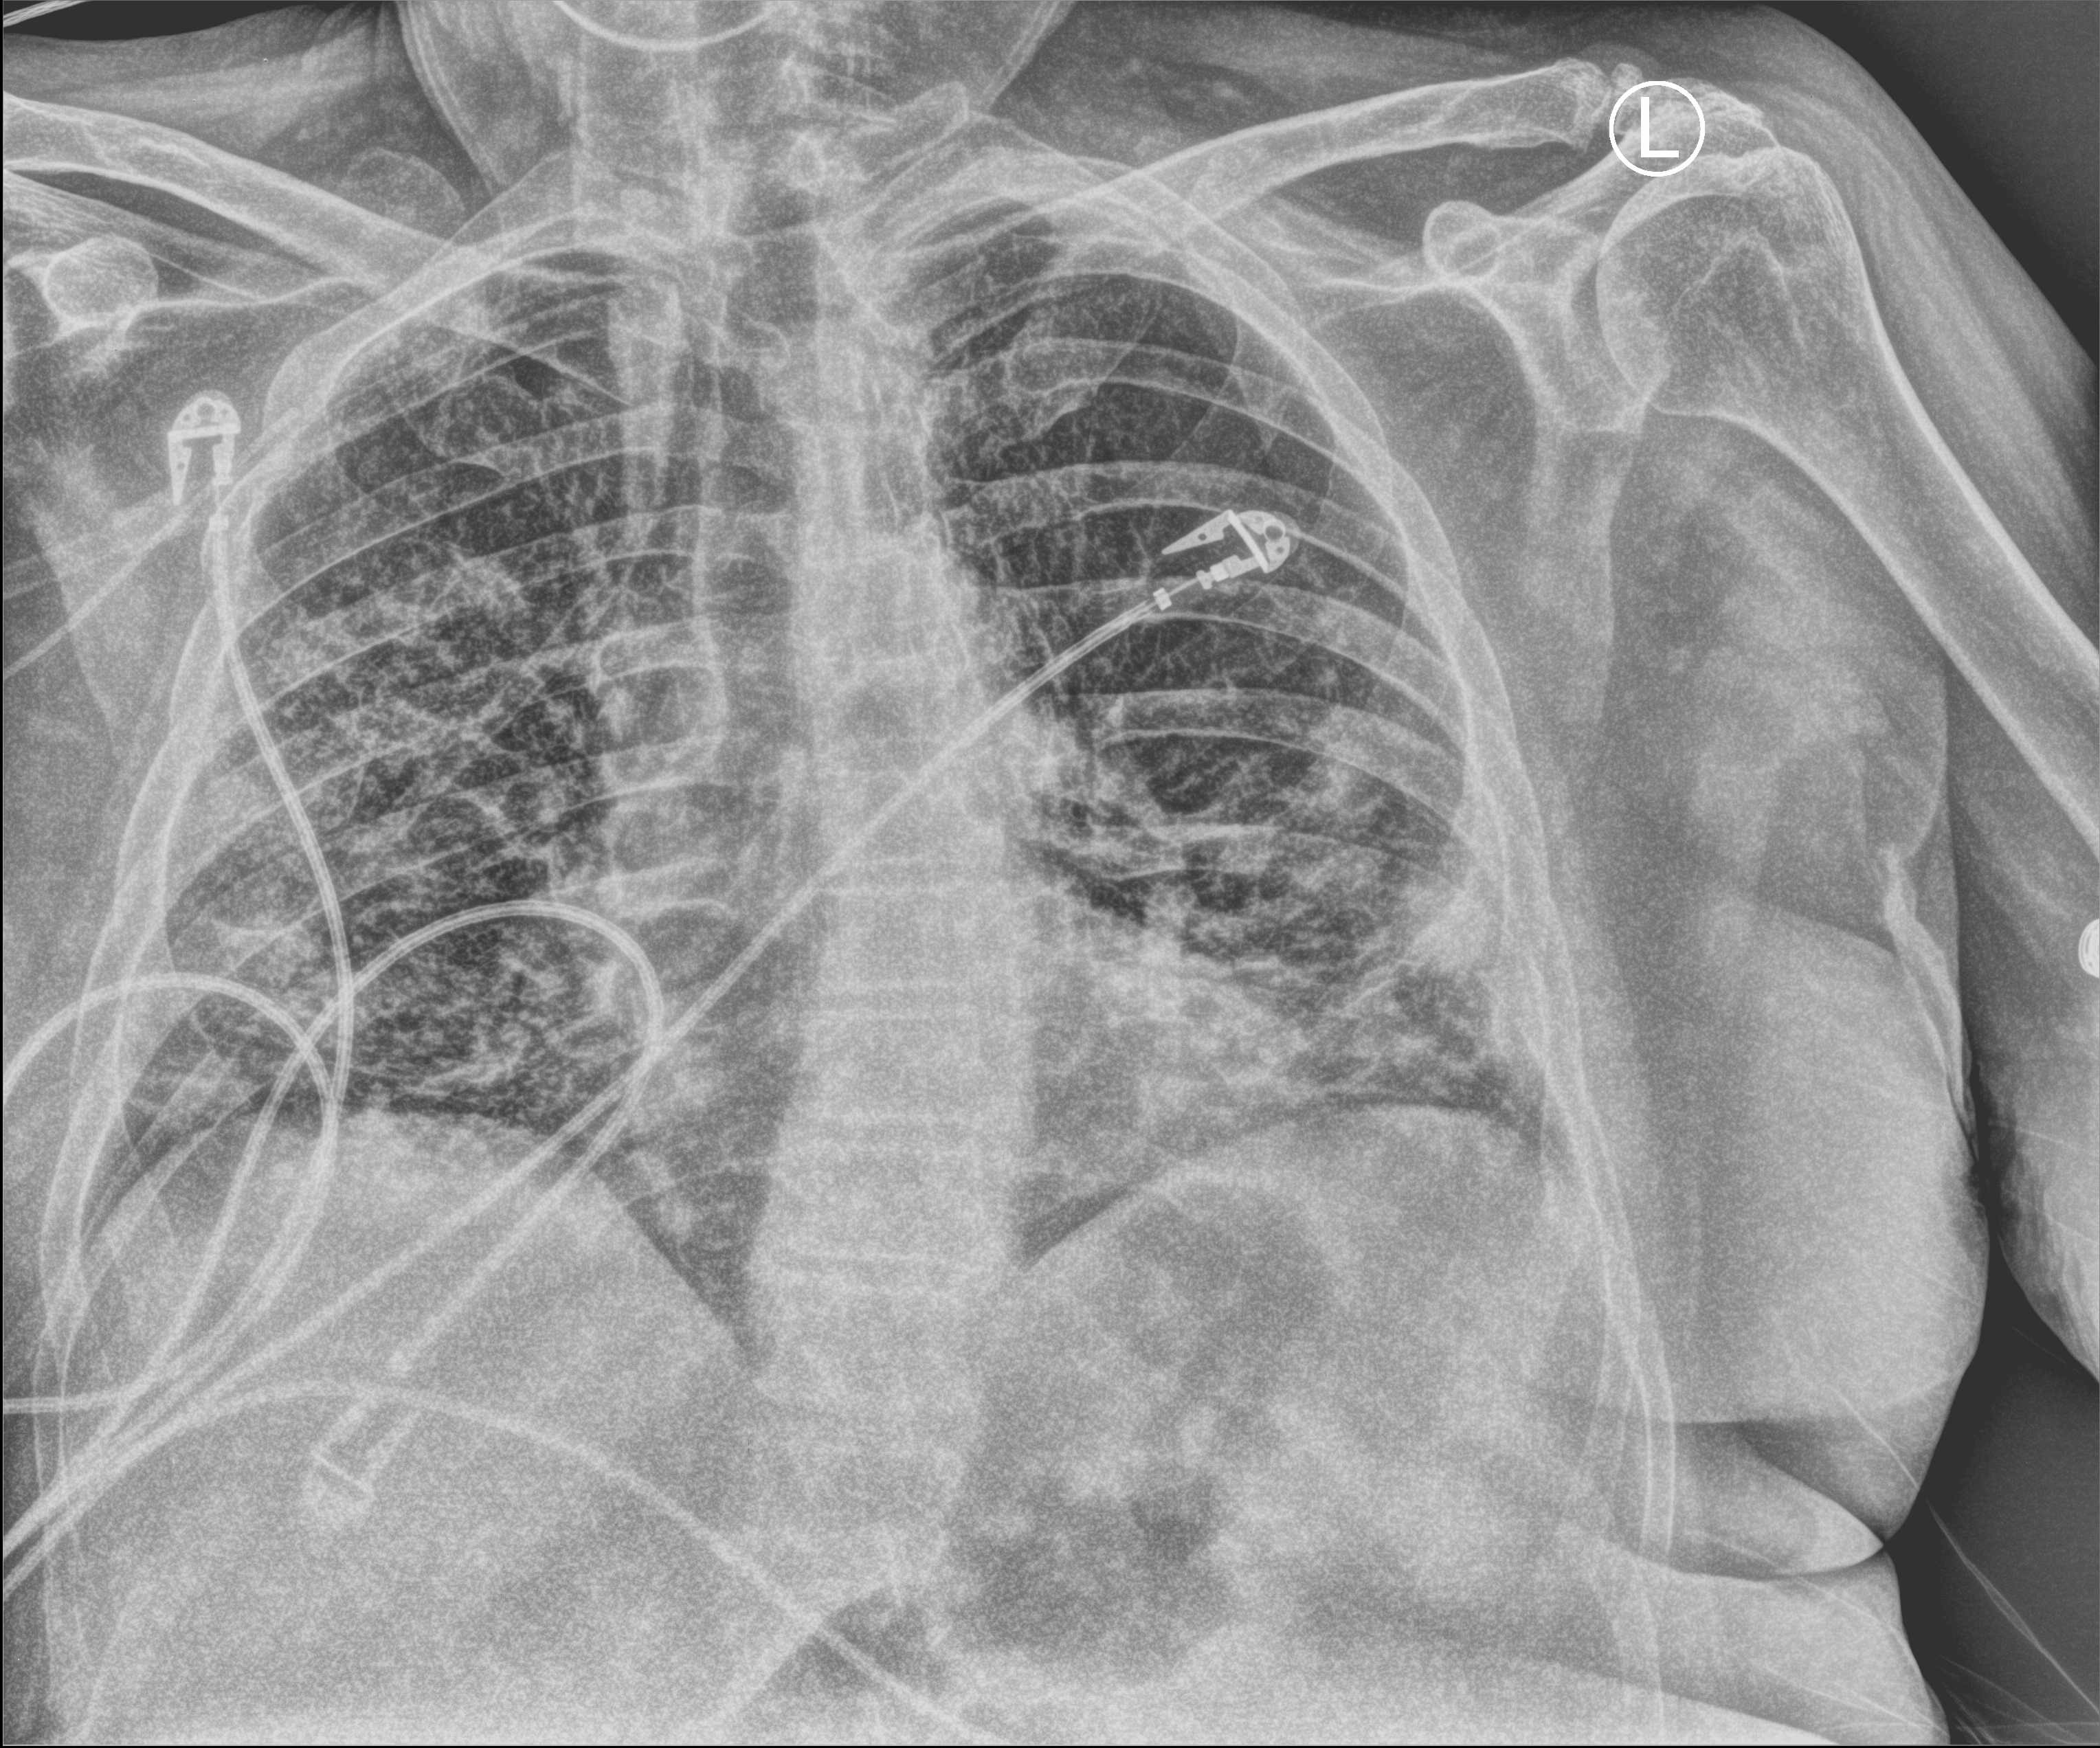
Bedside chest radiograph (computed radiography). Male patient hospitalised with COVID-19, age 60–74 years.
Admission-level facts for this patient (not findings on this image; timing relative to this image not recorded):
- admitted to intensive care during this hospital stay: no